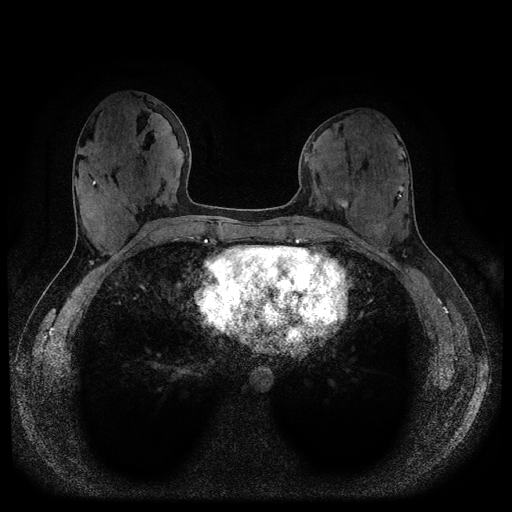
Breast MRI (dynamic contrast-enhanced, multi-phase), one axial slice. Slice 41 of 116 in the series (ordered by position). Dynamic contrast-enhanced series, time point 2 of 5 at this slice position (early post-contrast). 1.5 T. TE 2.6 ms, TR 5.3 ms. 2 mm slice thickness. 512 × 512 image matrix. Female patient, age 33 years.
Structures marked on this image (semi-automatically segmented with operator editing):
- breast lesion (labelled benign in the annotation): bounding box <335,194,349,212> (left, top, right, bottom; pixels)